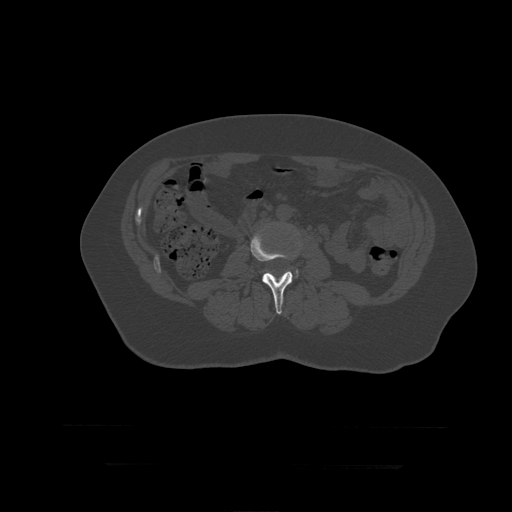
CT including the spine, one axial slice. Position 116 of 399 along the scan axis. Reconstruction kernel STANDARD. Bone window (W 1800 / L 400 HU). 1.25 mm slice thickness. 512 × 512 image matrix, field of view 450 × 450 mm. Patient age 41 years. From the clinical record (not read from this slice): primary cancer: breast.
Structures marked on this image (semi-automatic segmentation, software-assisted and operator-edited):
- L3 vertebra: box from (x=251, y=232) to (x=293, y=315) px
- L4 vertebra: (x=276, y=218)–(x=299, y=278)